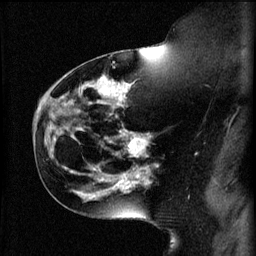
Breast MRI (dynamic contrast-enhanced), one sagittal slice. Slice 36 of 60 in the series (ordered by position). 3 images stored at this slice position (order not interpretable as contrast timing). 1.5 T. TE 4.2 ms, TR 11 ms. 256 × 256 image matrix. Patient: female, 44 years.
Outlined on this slice (semi-automatic segmentation, software-assisted and operator-edited):
- analysis volume of interest (the breast-tissue region the enhancement analysis was run in; not a lesion): bounding box <110,130,159,179> (left, top, right, bottom; pixels)
- tumour enhancement mask (voxels above the 70 % enhancement threshold inside the analysis volume of interest): <116,130,151,179>